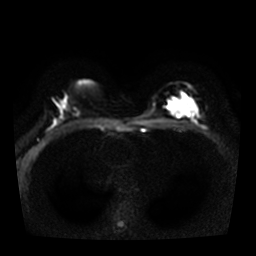
Breast MRI, one axial slice; slice 19 of 36 in the series (ordered by position); diffusion-weighted series; image 2 of 4 stored at this slice position (different b-values; order by instance number); 3 T; 256 × 256 image matrix. Female patient.
Outlined on this slice (manually delineated by an expert):
- tumour on diffusion-weighted imaging: bounding box [x1, y1, x2, y2] px = [168, 94, 197, 117]